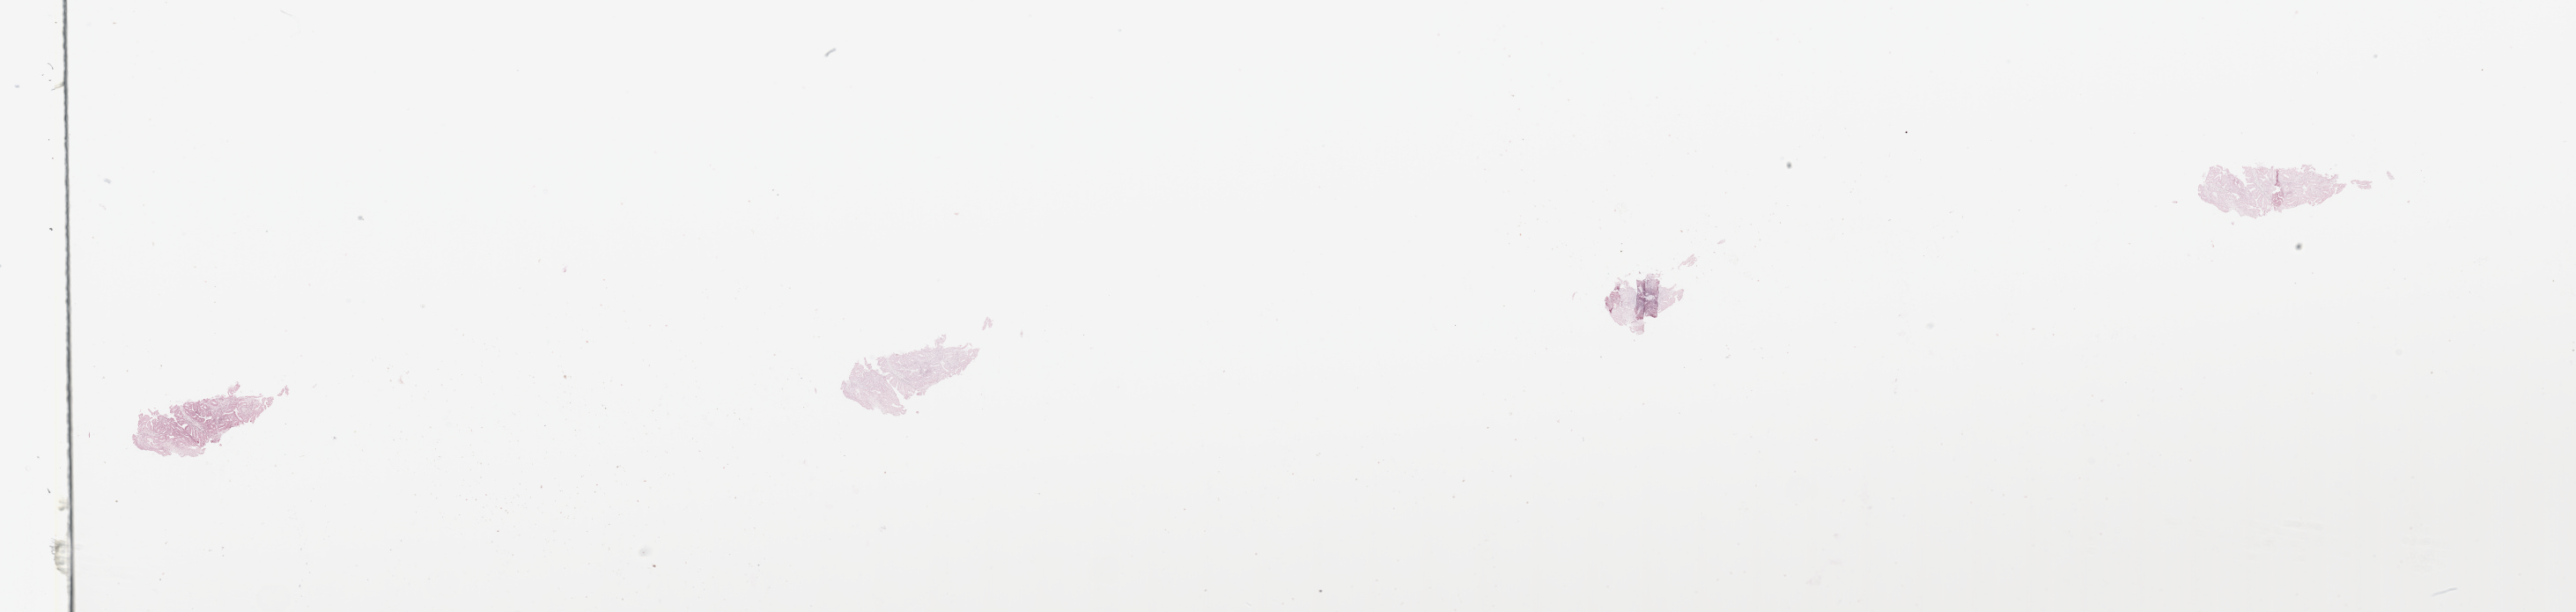
Digitized H&E-stained tissue section (whole slide) — a low-resolution overview of the entire scanned area, about 46.3 x 11.0 mm (slide scanned at 20x); tumour tissue sample, sampled site: uterus. Female, 75 y/o. Histologic grade: G1 (well differentiated). Pathologist review of this section (percent, as recorded): tumour nuclei 80%, necrosis 0%.
AJCC pathologic stage: I. Diagnosis: Endometrioid adenocarcinoma, NOS.